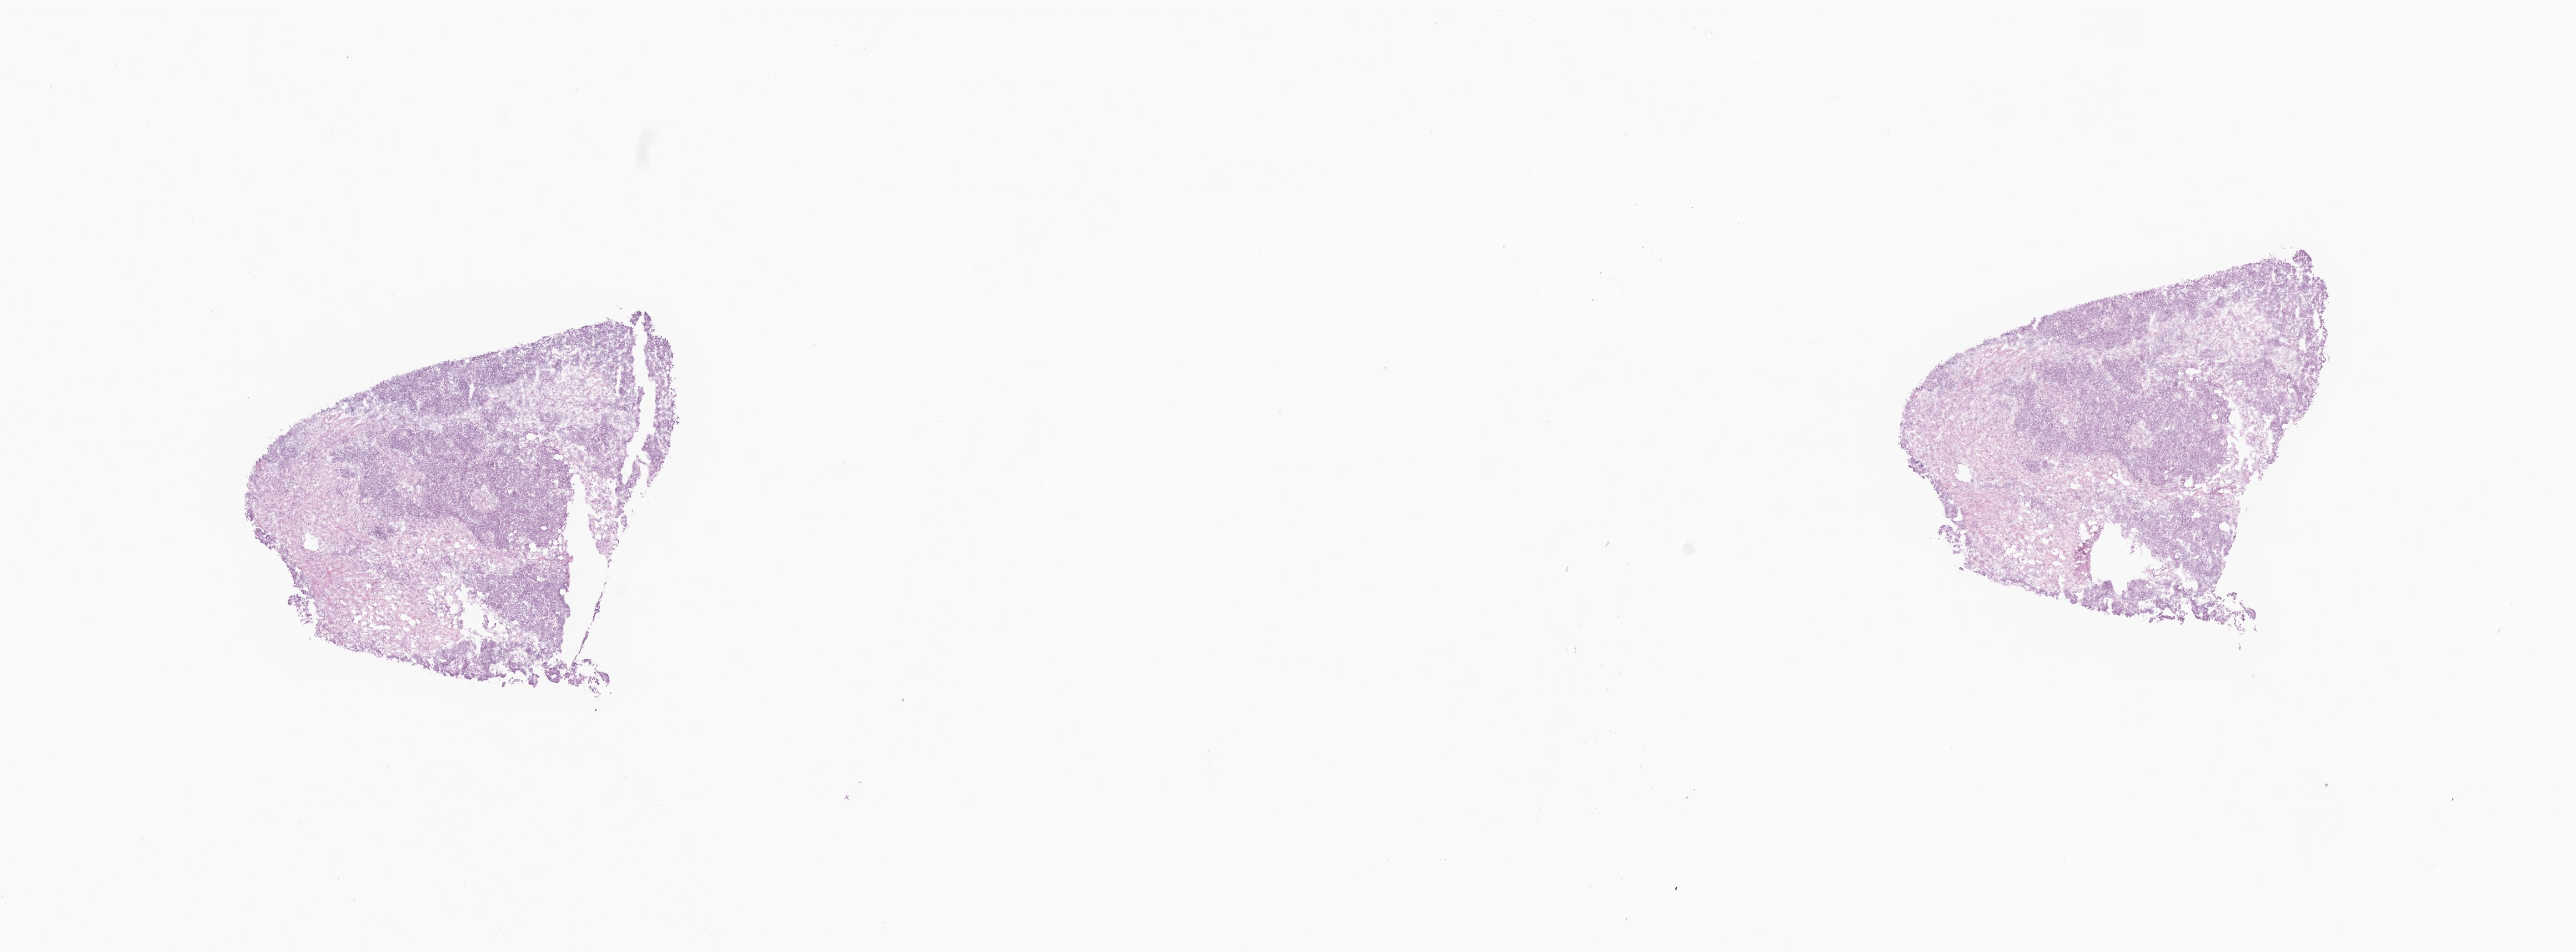
Whole-slide image, hematoxylin and eosin (H&E) stain, a low-resolution overview of the entire scanned area, about 19.5 x 7.2 mm, frozen section (tissue freezing medium), metastatic tumor tissue, resected from specified parts of peritoneum. Female, age 62 years at initial diagnosis. Composition of this section per pathologist review: tumor cells 45%, tumor nuclei 45%, stromal cells 40%, necrosis 0%, normal cells 15%. Inflammatory infiltration, as recorded: lymphocyte infiltration 5%, monocyte infiltration 2%, neutrophil infiltration 0%.
- section: bottom of the tissue portion
- patient diagnosis (primary): Carcinoma, metastatic, NOS